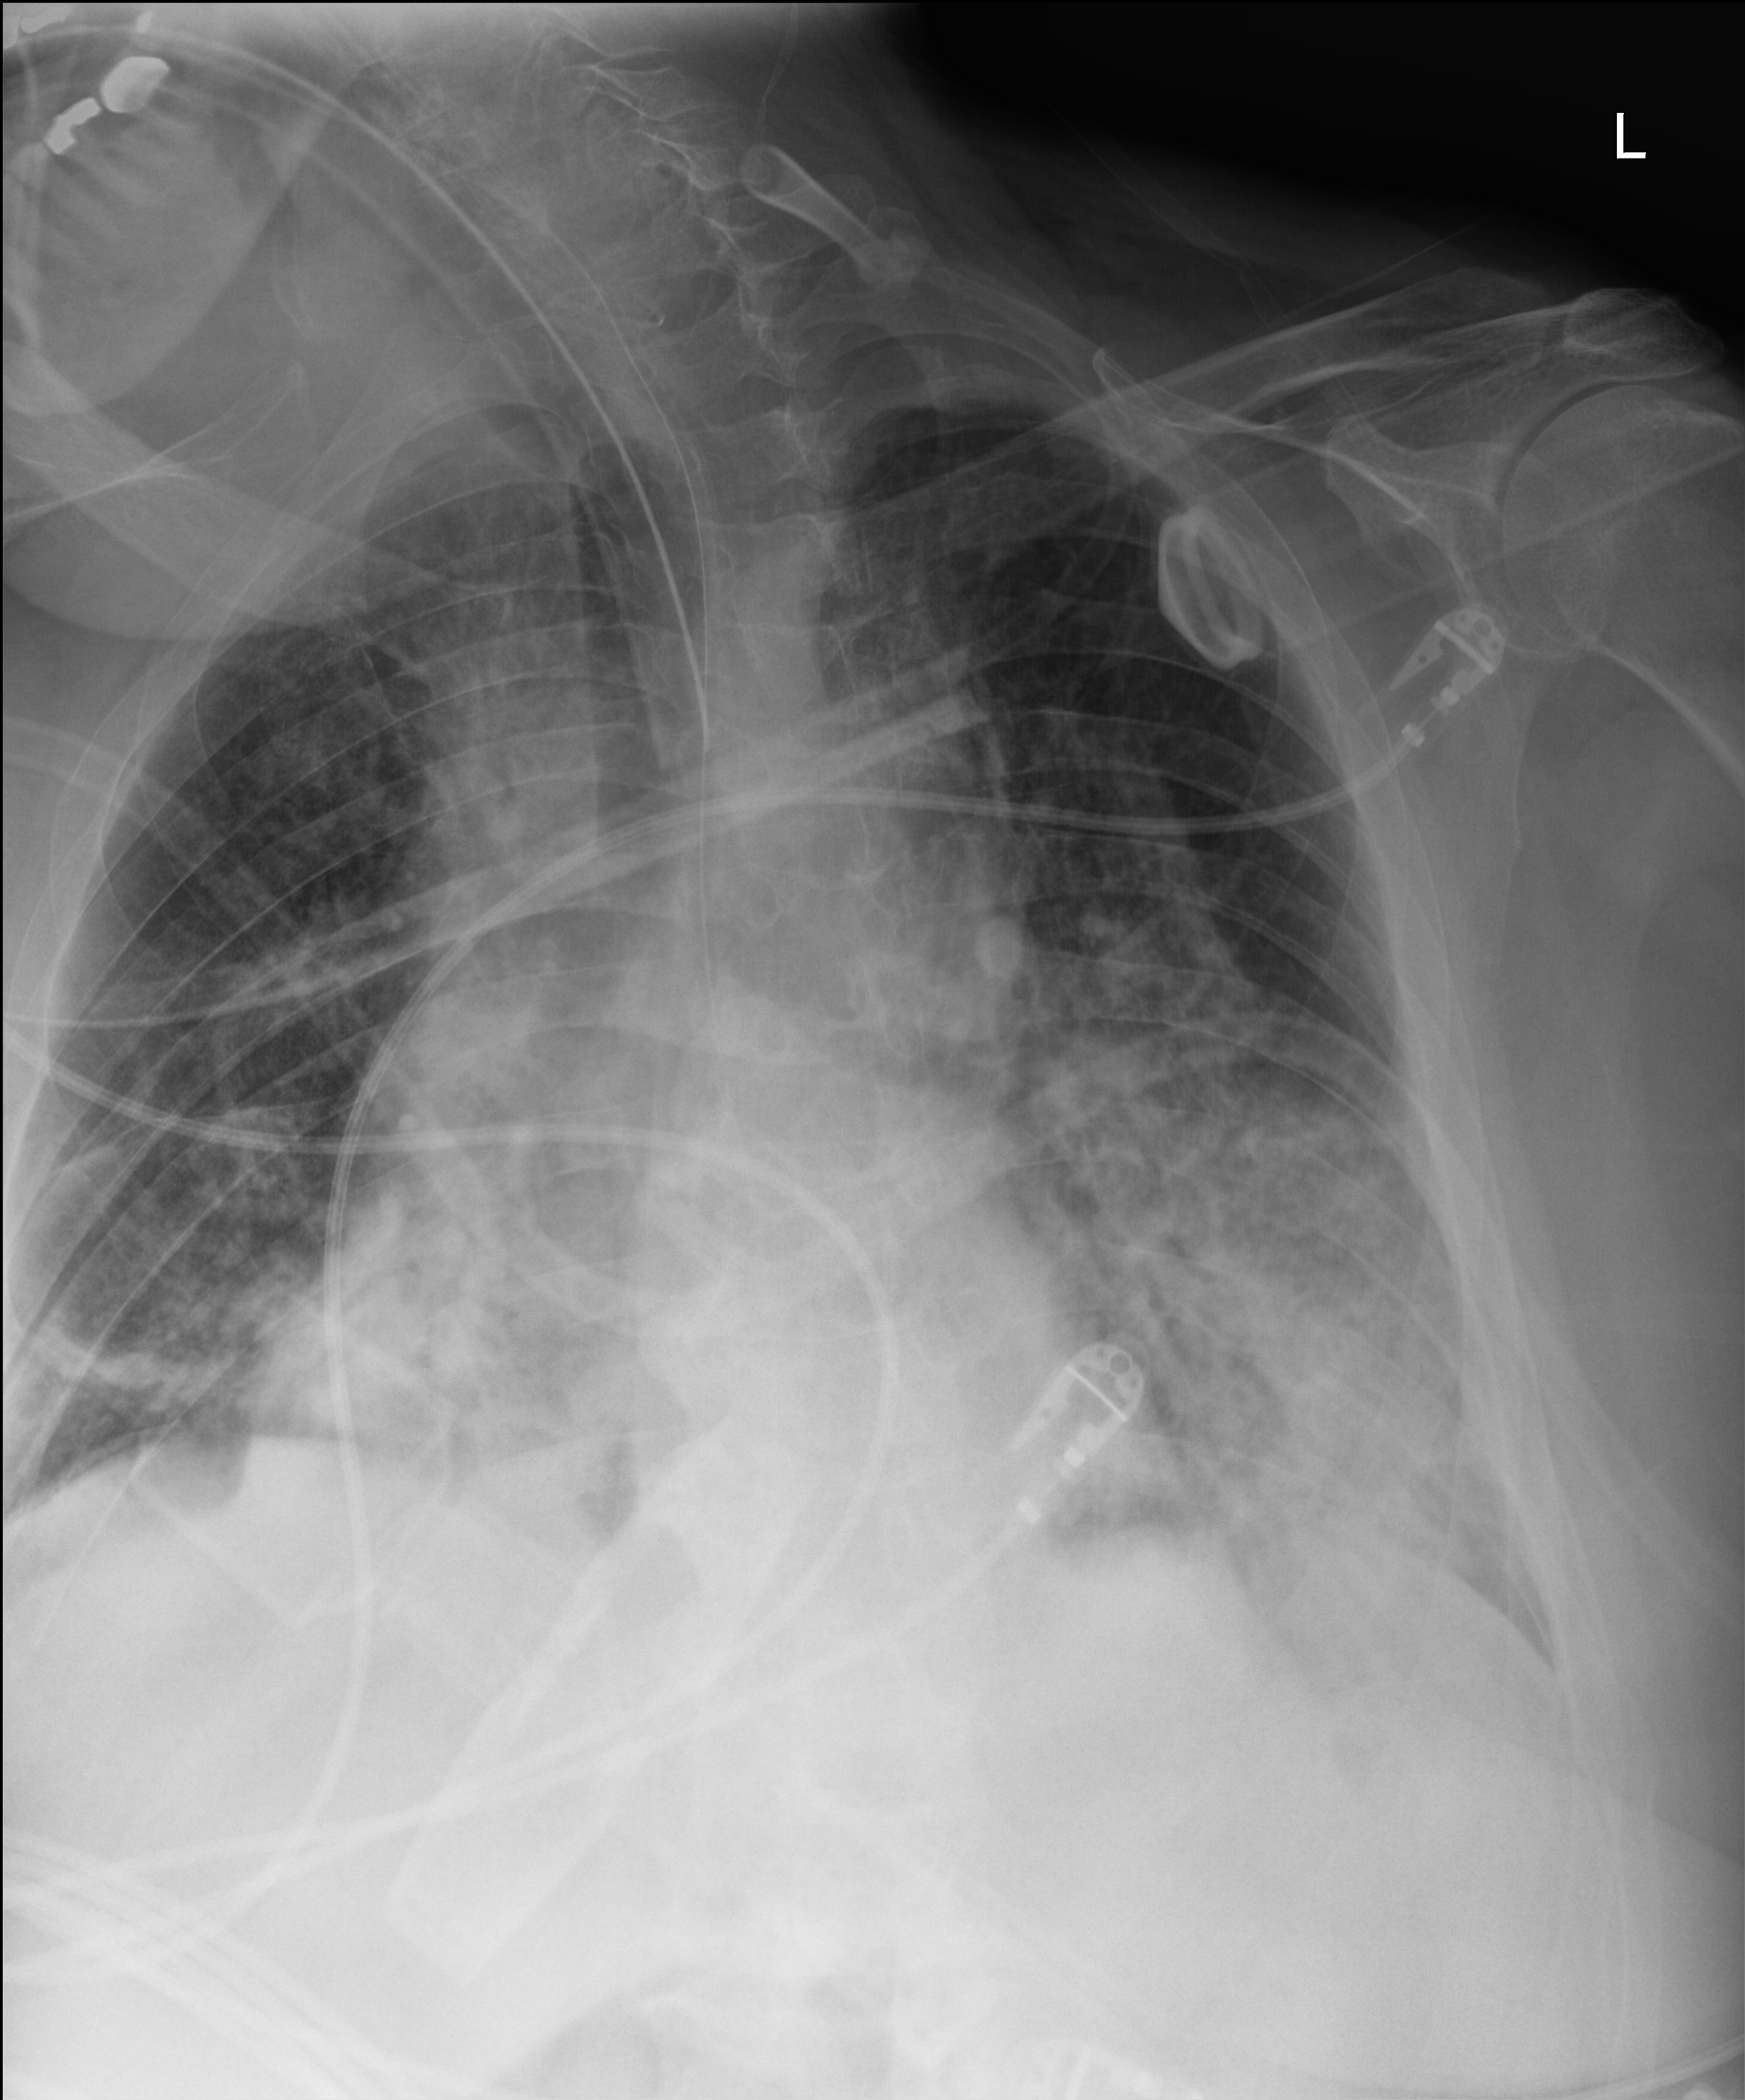
Chest radiograph; anteroposterior (AP) projection. Male patient hospitalised with COVID-19, age 60–74 years.
From the hospital-stay record, not from the radiograph (when in the stay this image was taken is not recorded): admitted to intensive care during this hospital stay: yes.